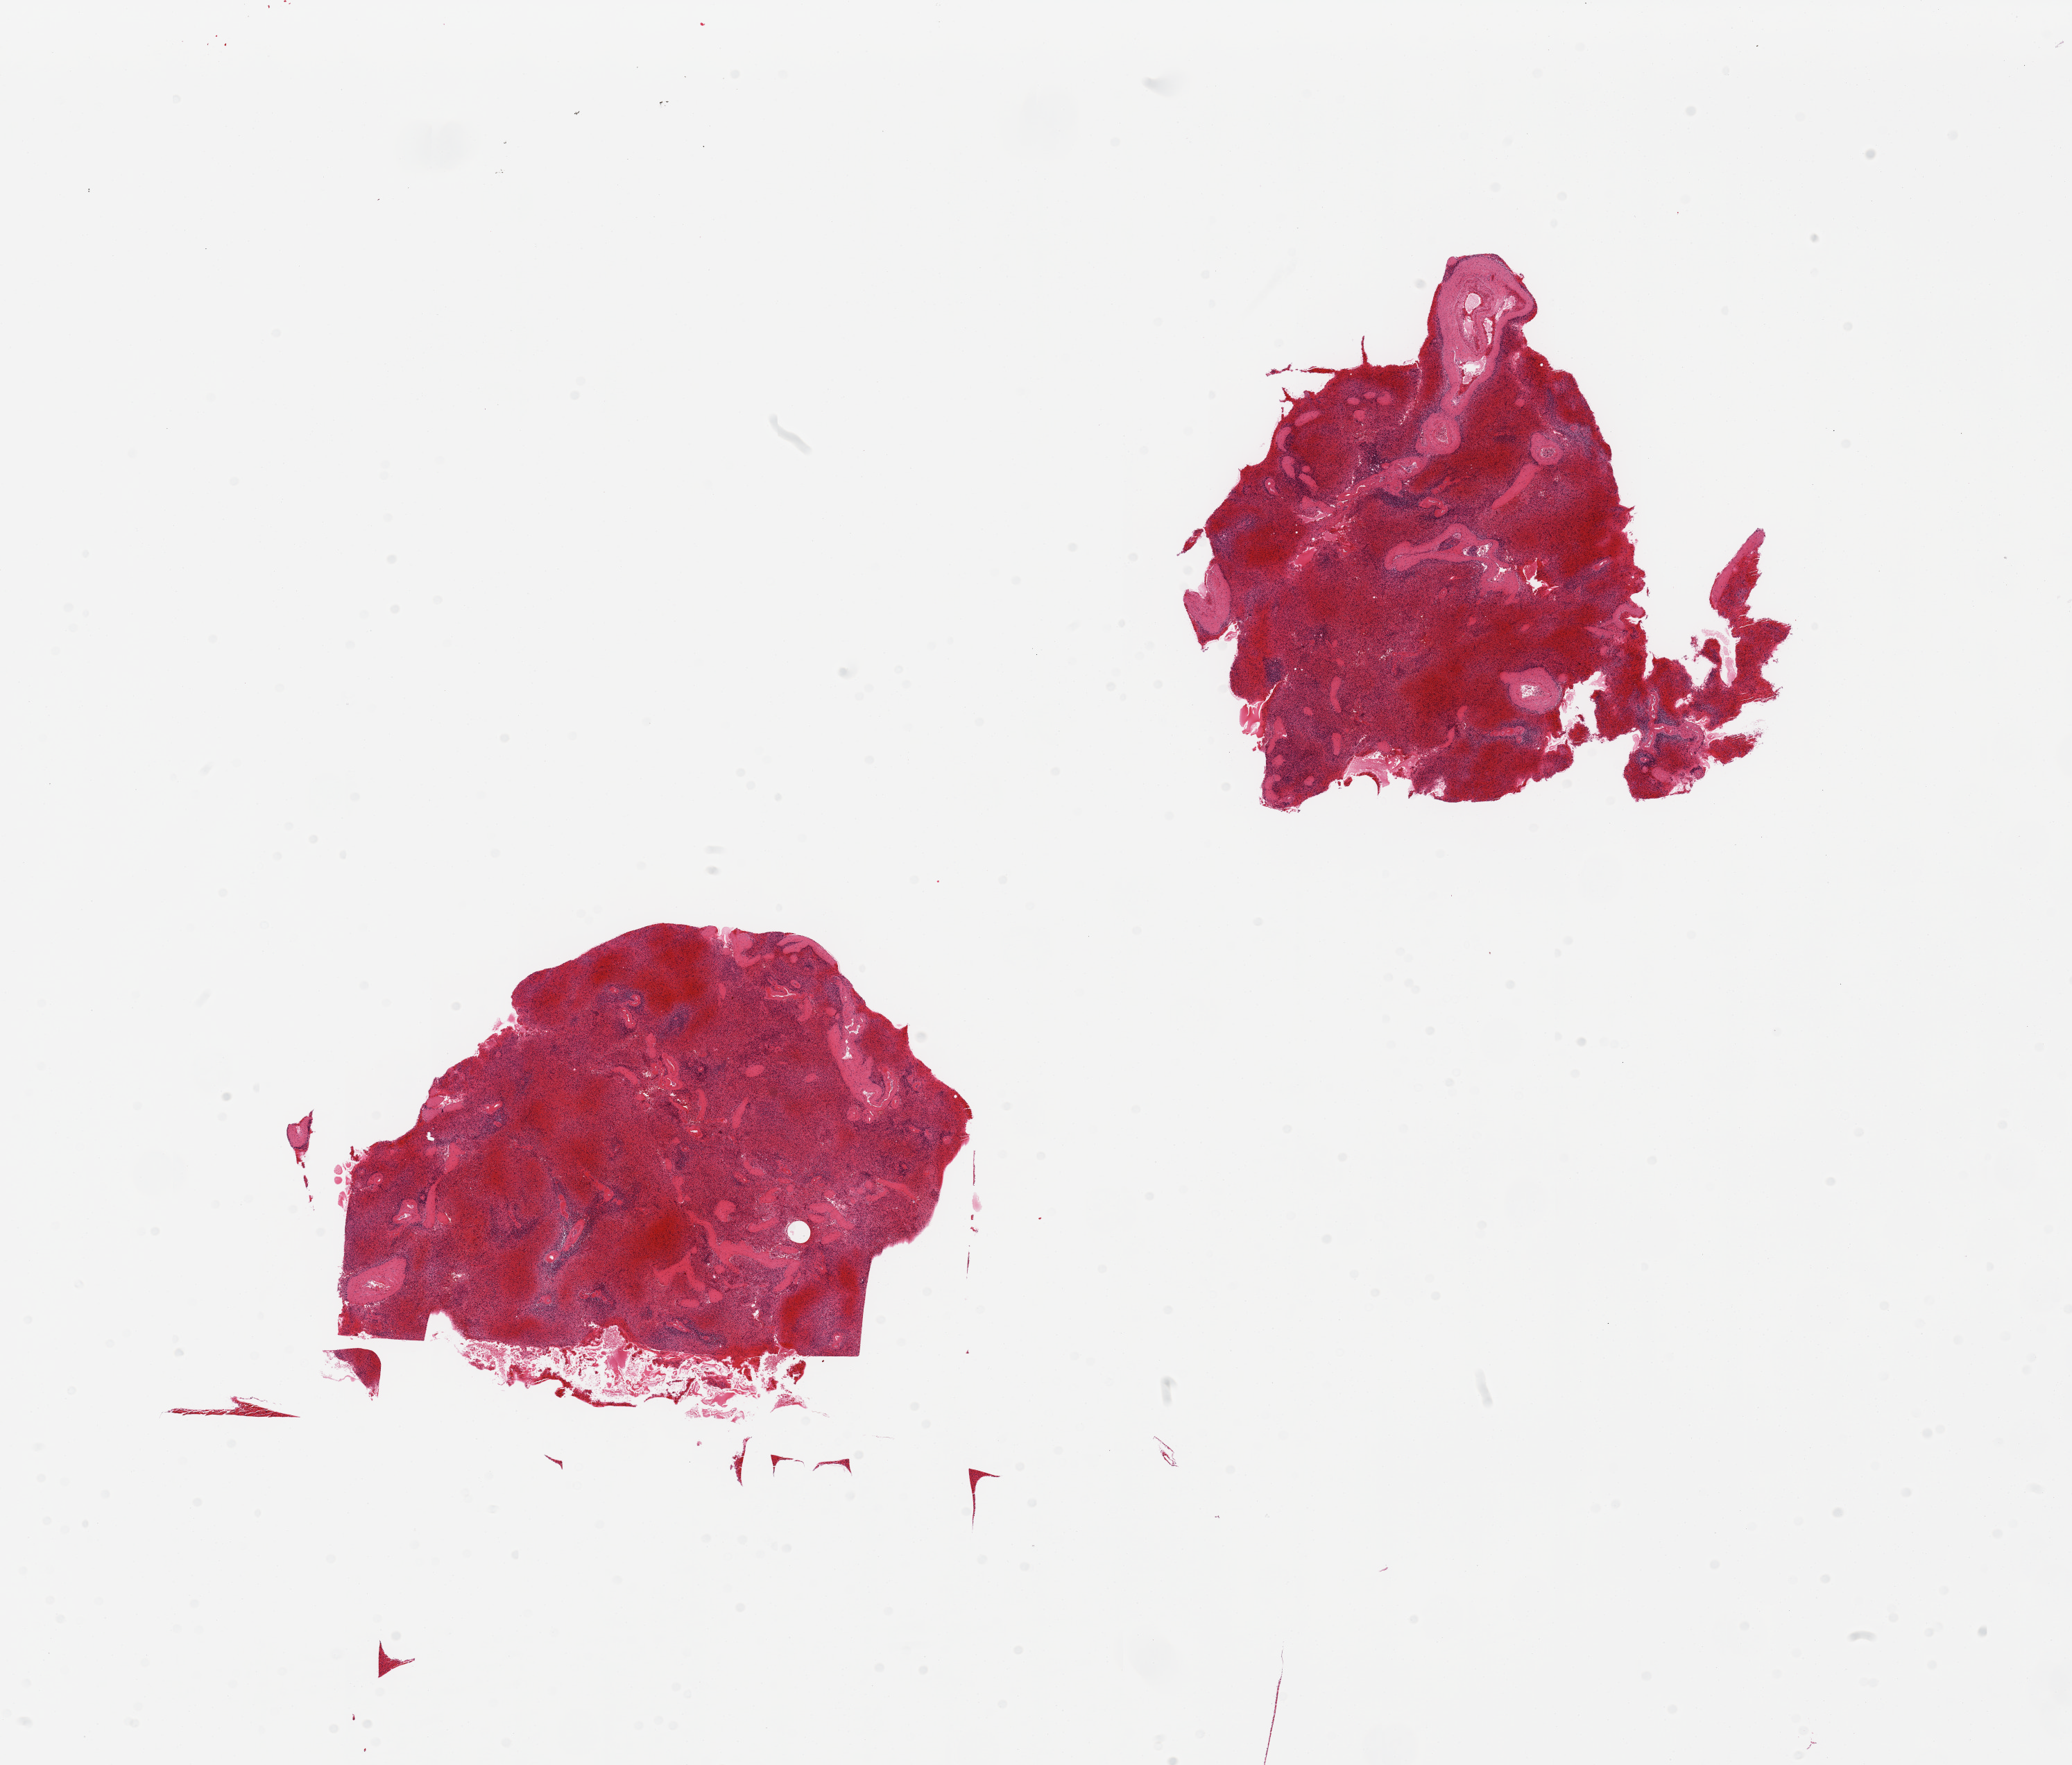
Whole-slide image, haematoxylin and eosin stain — a low-resolution overview of the entire scanned area, about 23.6 x 20.1 mm (acquisition: 20x scan). PAXgene-fixed paraffin-embedded (PFPE) section. Section of spleen (target tissue). Donor tissue sample.
Reviewer comment on this tissue sample: 2 pieces, marked congestion.